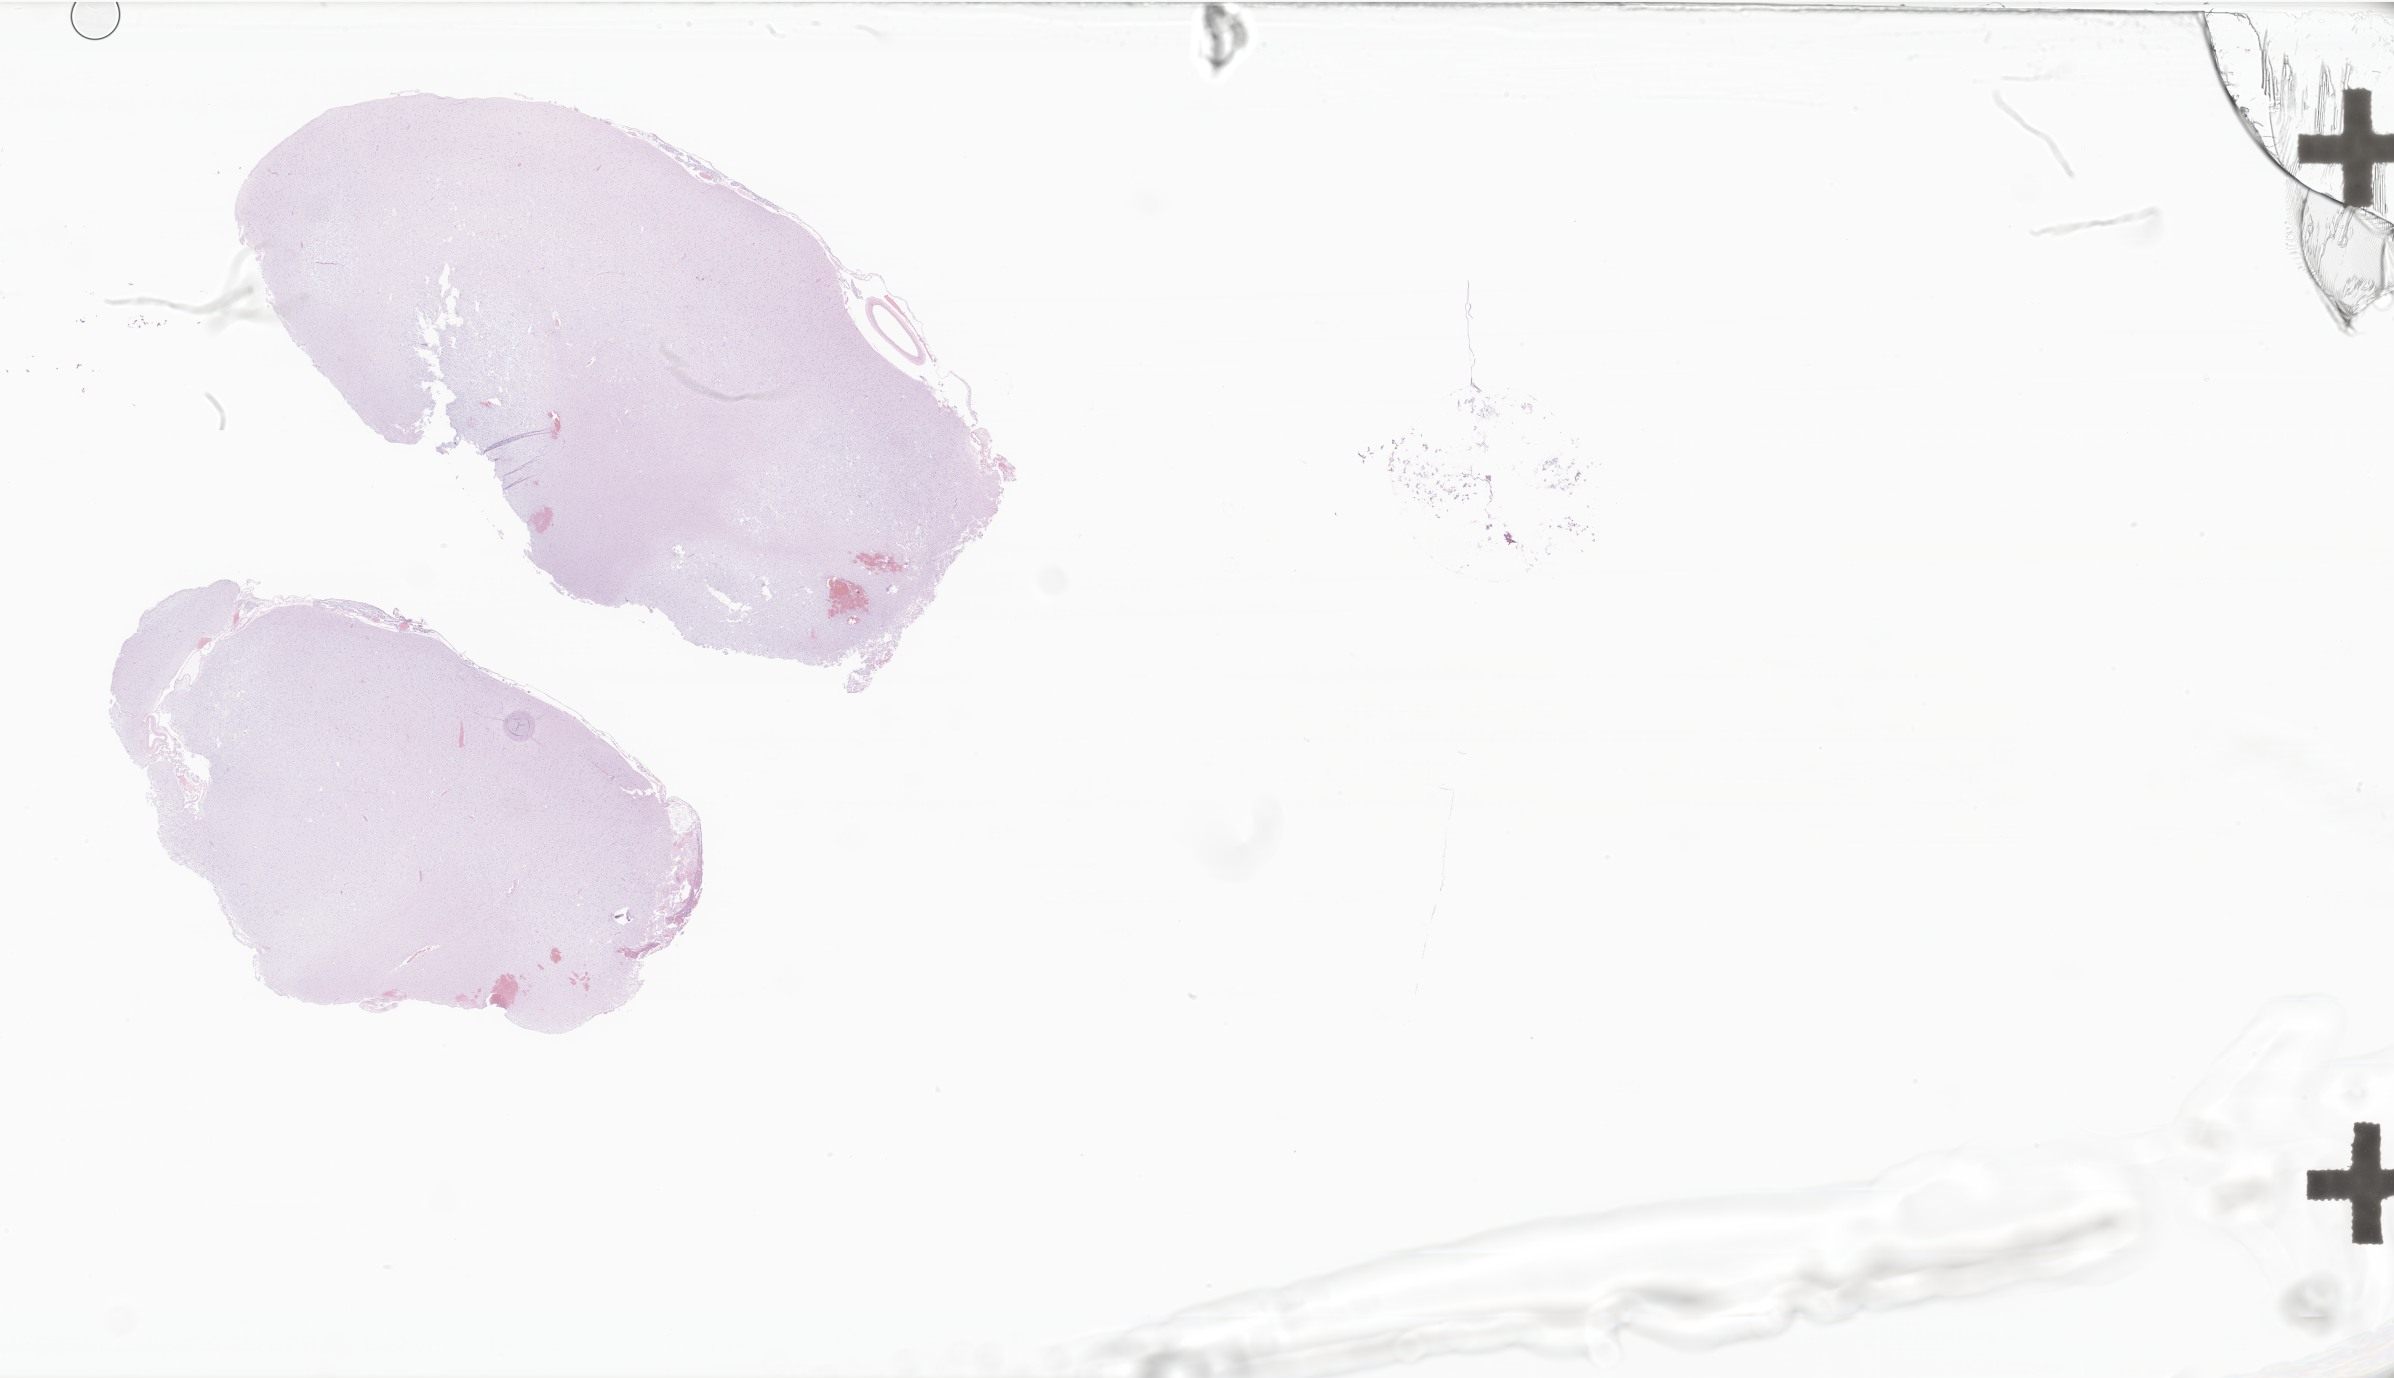
Digitized hematoxylin and eosin (H&E)-stained section of tumor tissue from the frontal lobe — shown as a low-resolution overview of the whole scanned area (about 40.4 x 23.2 mm). Formalin-fixed paraffin-embedded section. Female patient, age 207 months (17 years 3 months).
Diagnosis: Glioma, malignant.